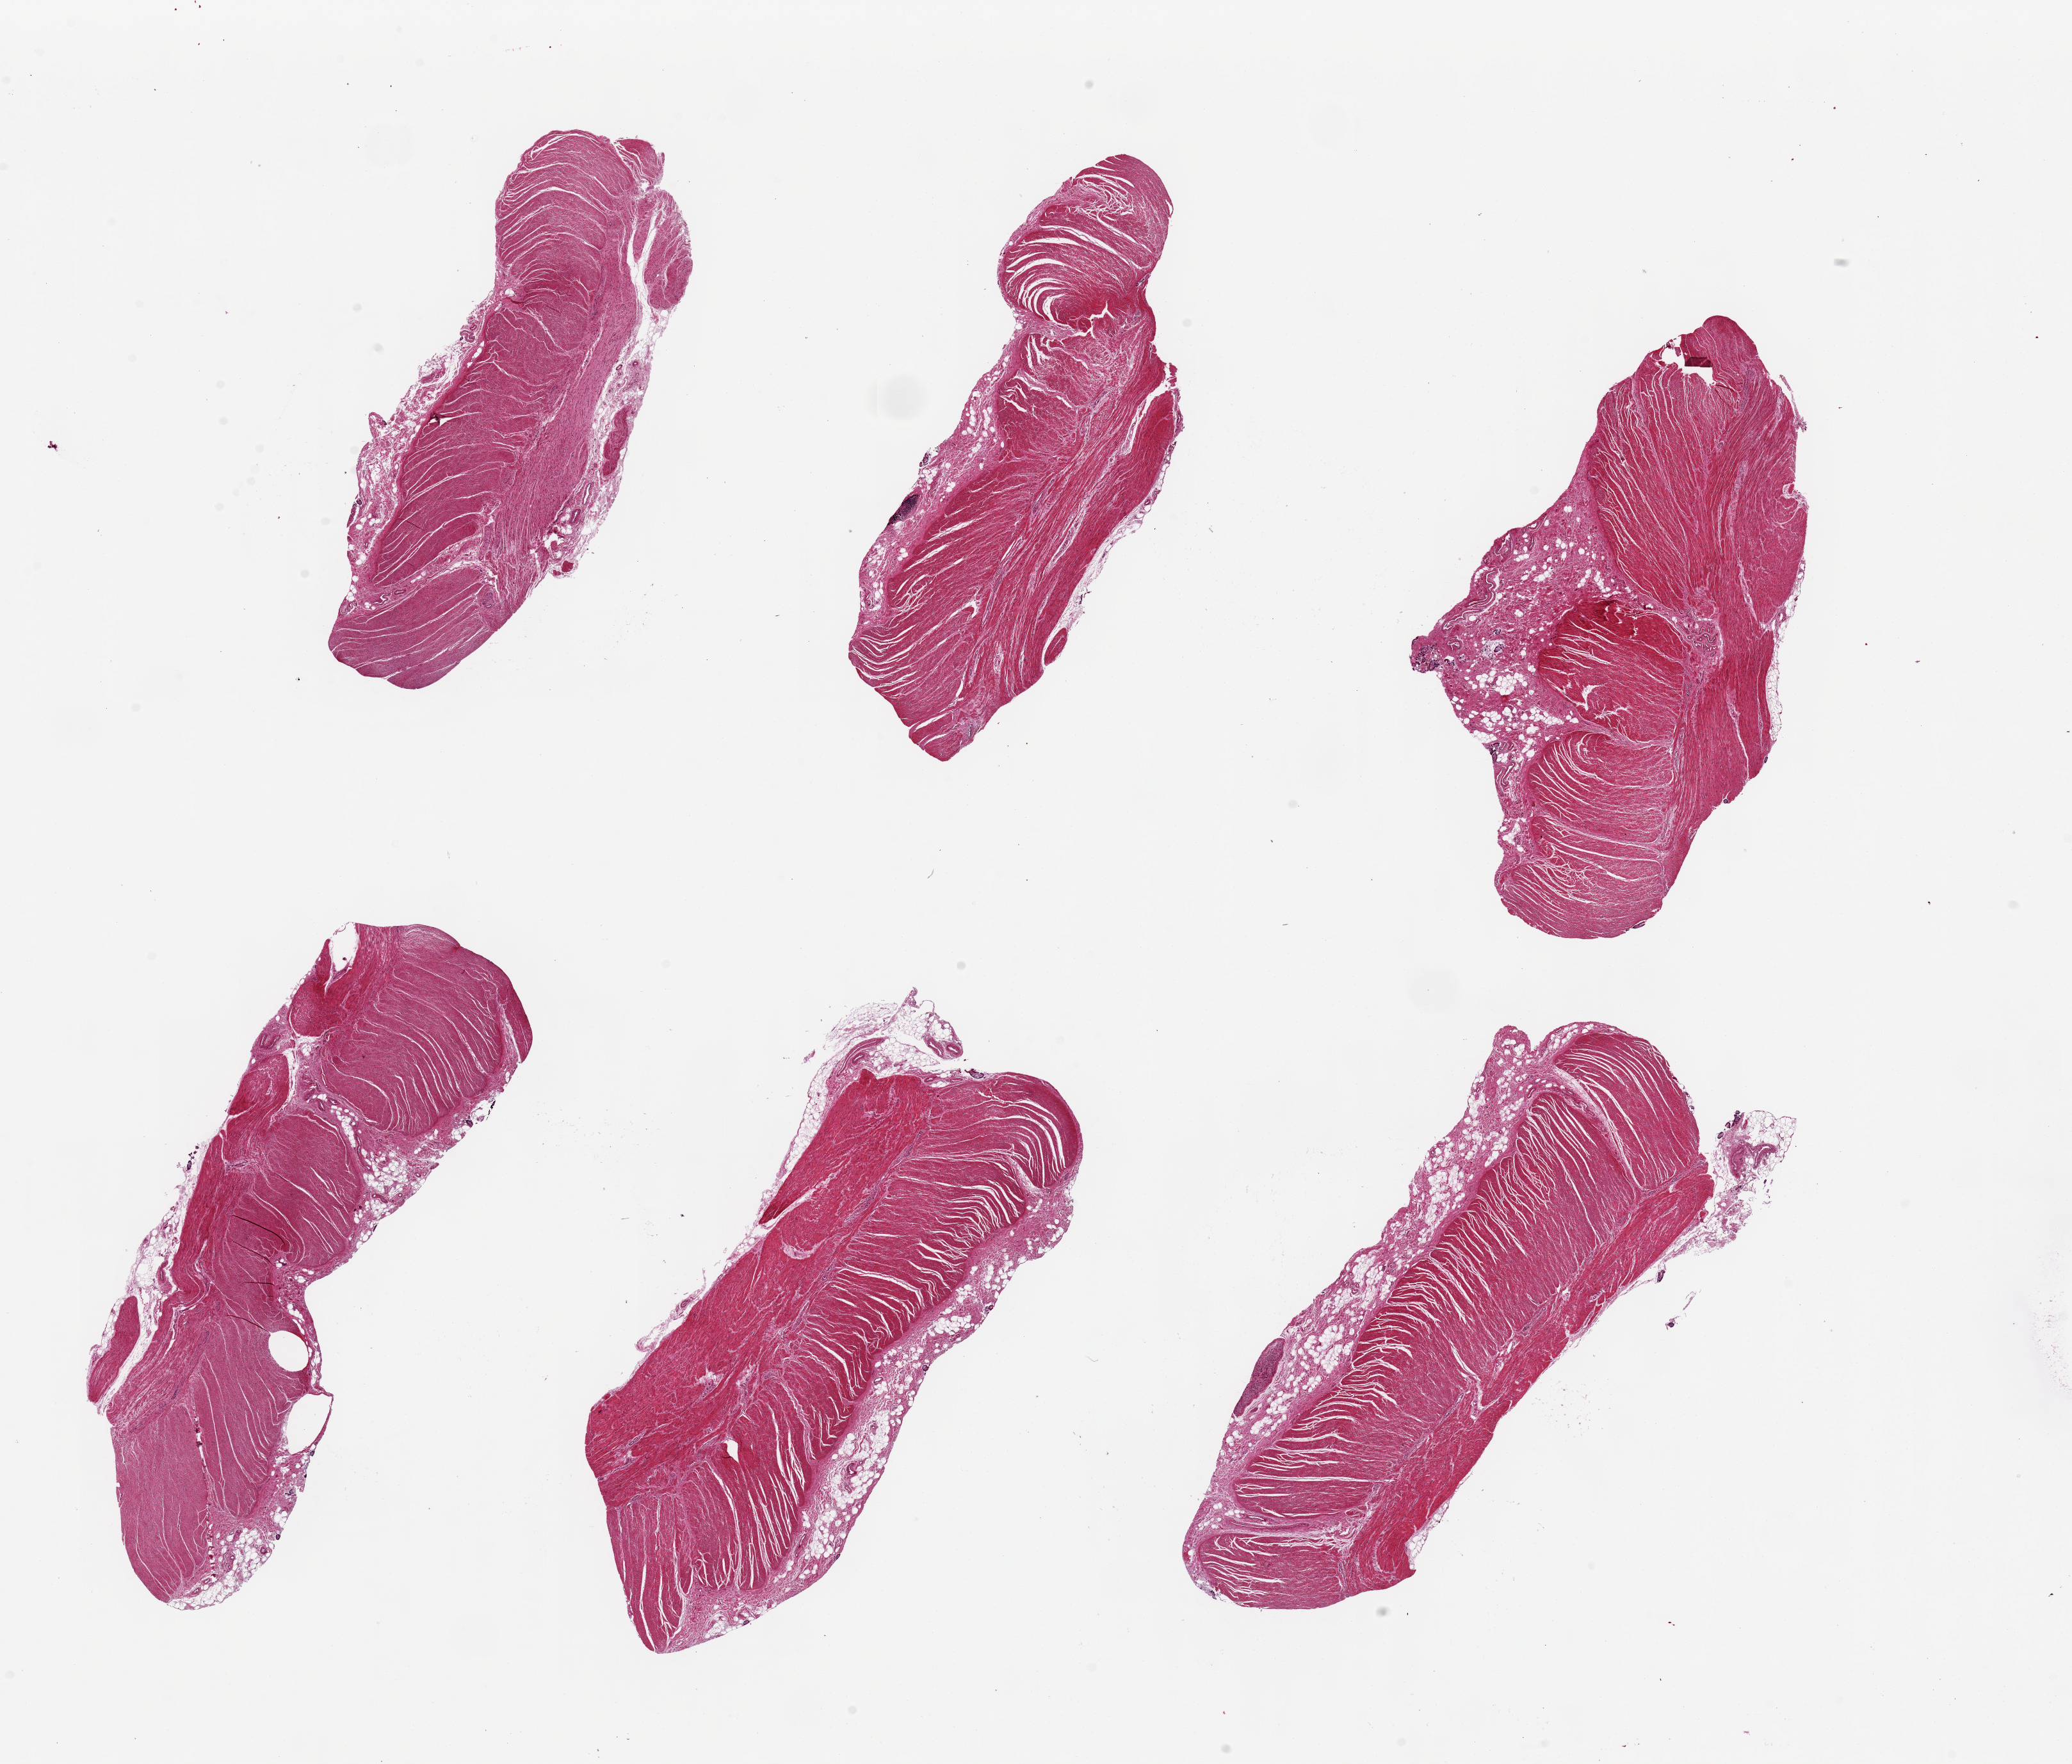
Digitized H&E-stained section, brightfield — whole scanned area (about 25.6 x 21.8 mm) shown as a low-resolution overview. PAXgene-fixed, paraffin-embedded tissue. Section of sigmoid colon (target tissue). Tissue donor sample. Donor sex: female.
Reviewer comment on this tissue sample: 6 pieces, up to 9x4mm. Well trimmed muscularis except for up to 1 mm submucosa in all.